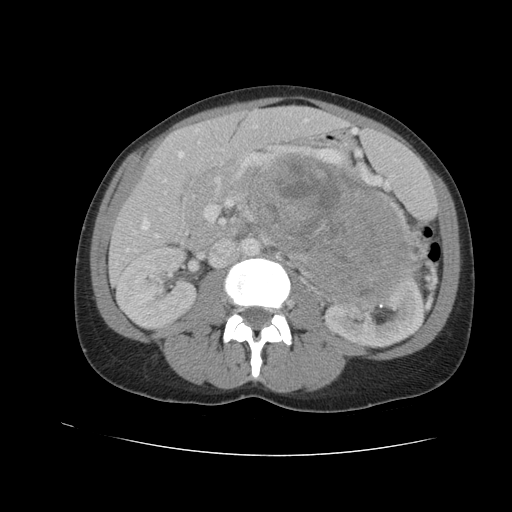
Contrast-enhanced abdominal CT, one axial slice. Position 54 of 90 along the scan axis. Reconstruction kernel STANDARD. Intravenous contrast given. Soft-tissue window (W 400 / L 40 HU). 512 × 512 image matrix, field of view 360 × 360 mm. Female patient. From the clinical record (not read from this slice): diagnosis: adrenocortical carcinoma; tumour side: left adrenal; tumour size at pathology: 18 cm; Ki-67 index: 11 %; stage (as recorded): 3.
Structures marked on this image (semi-automatic segmentation, software-assisted and operator-edited):
- mass: bounding box (x1, y1, x2, y2) in pixels: (251, 154, 419, 300)